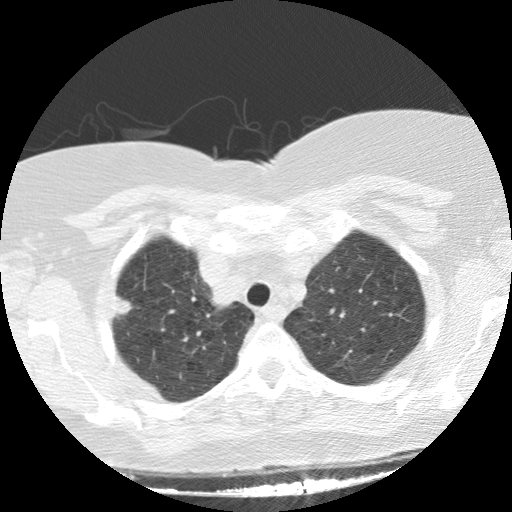
Low-dose screening chest CT, one axial slice; position 114 of 136 along the scan axis; 120 kVp; lung window (W 1500 / L -600 HU); 2.5 mm slice thickness; 512 × 512 image matrix.
Annotated regions visible in this slice (manually delineated by an expert):
- lesion 1 (tumor, upper lobe of right lung): bounding box [x1, y1, x2, y2] px = [116, 296, 133, 316]